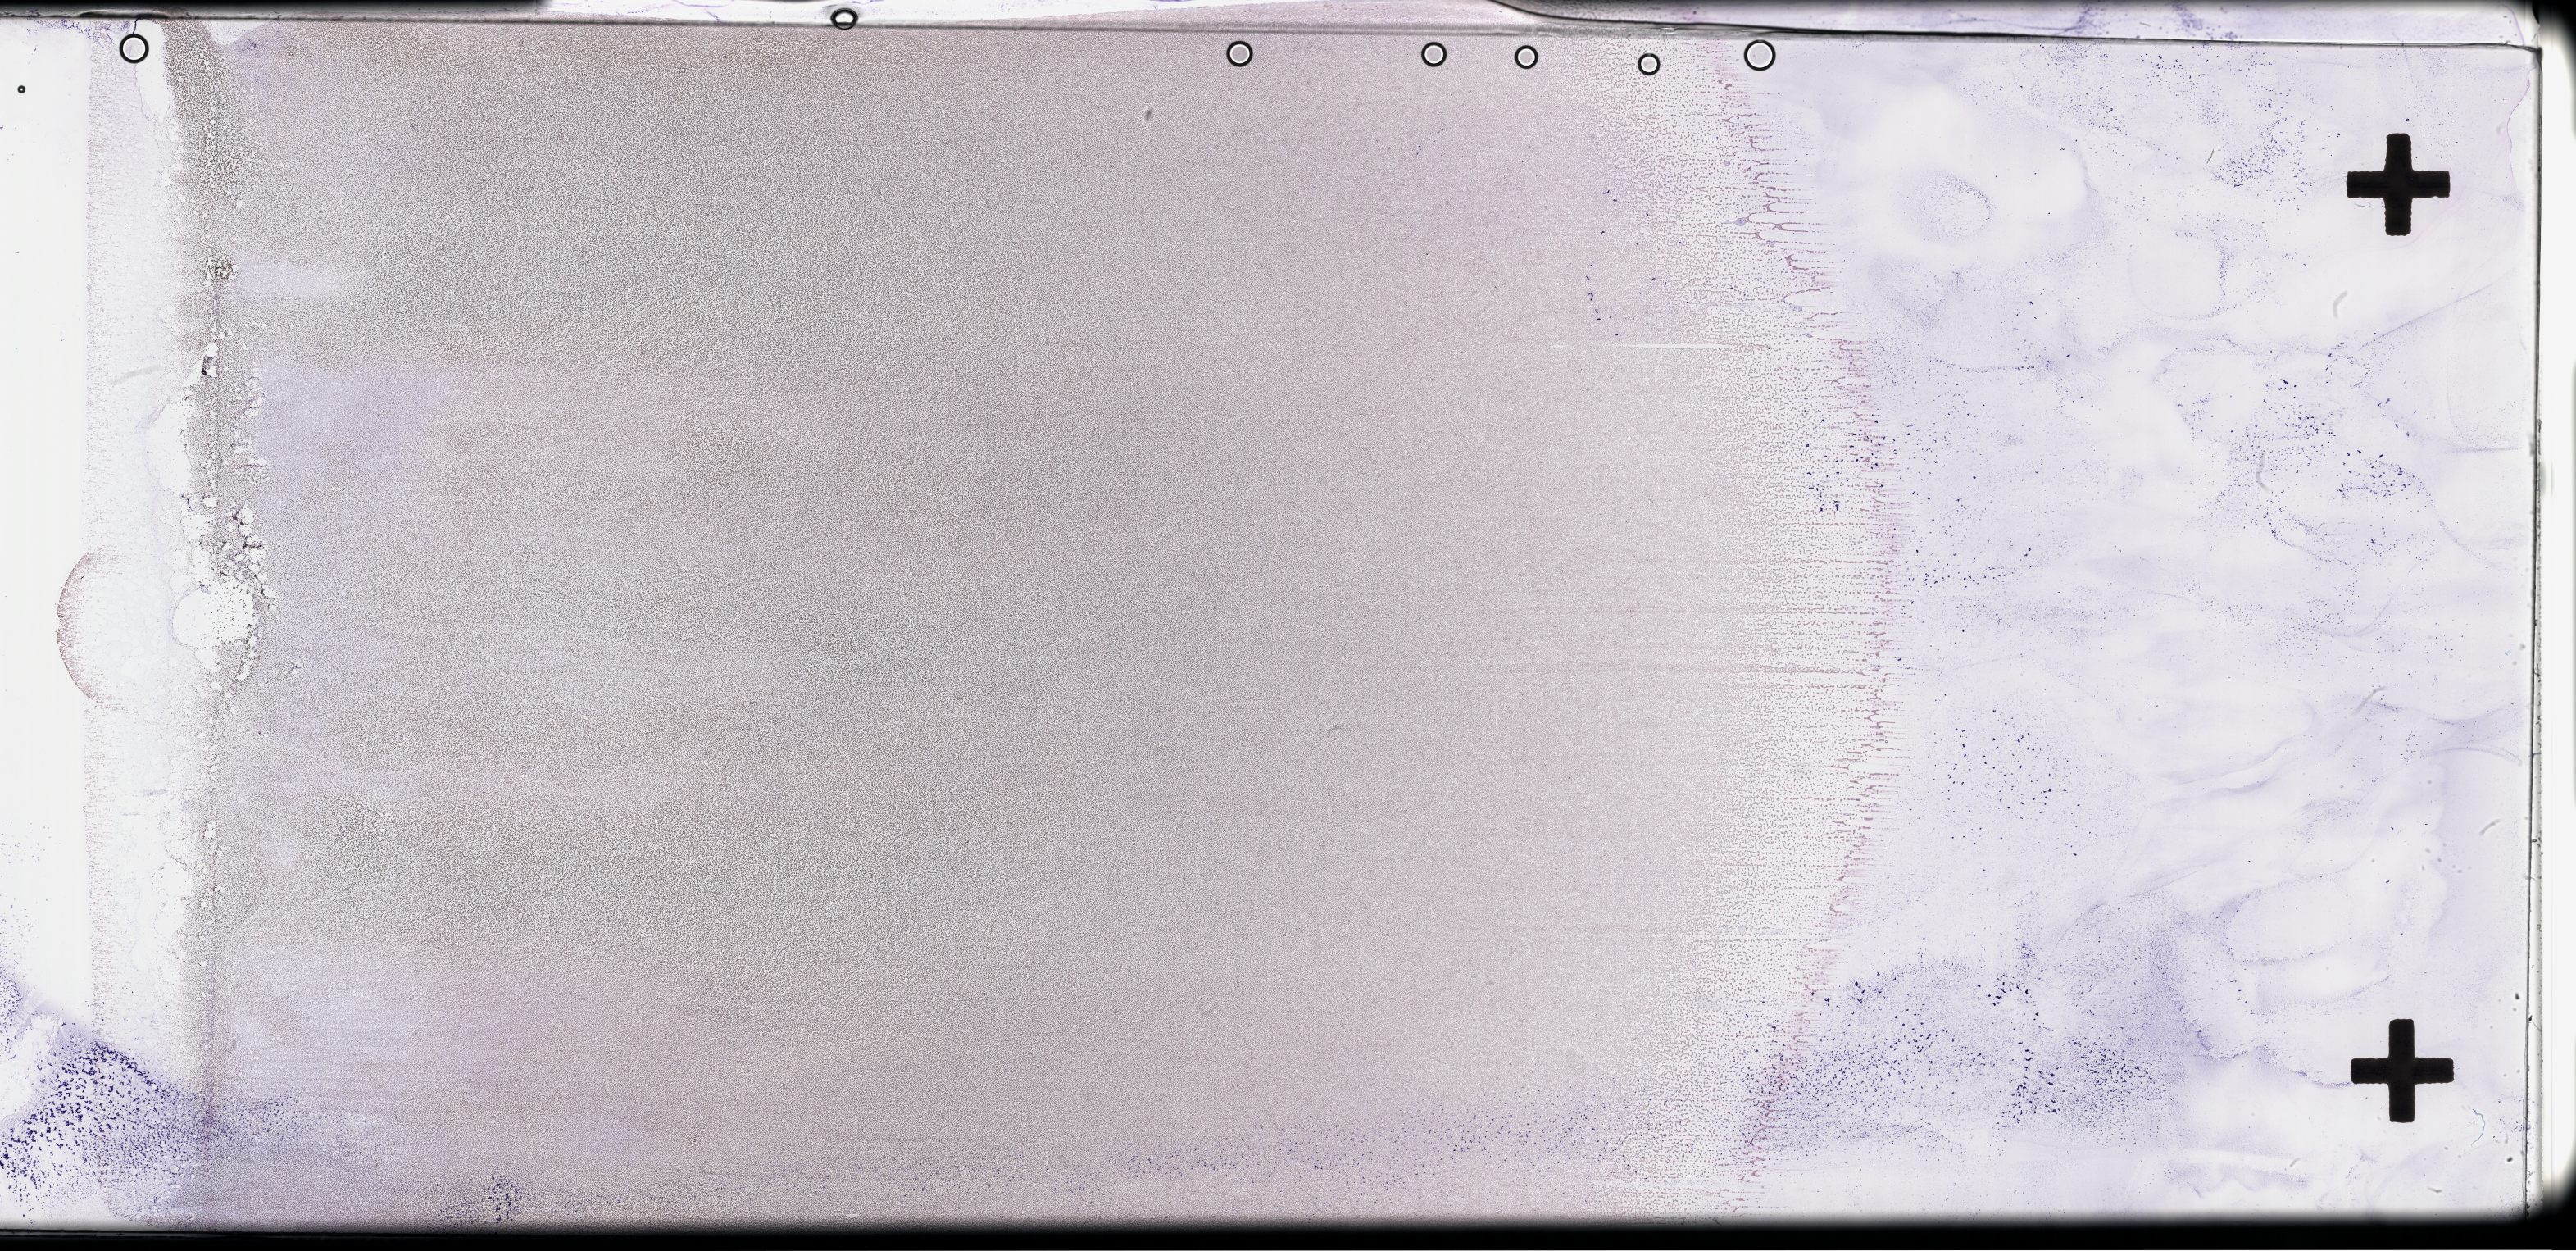
Wright–Giemsa-stained whole blood smear, whole-slide image — low-resolution overview of the scanned area, about 50.8 x 24.6 mm. Smear from an EDTA sample. Specimen time point: collected at baseline (before treatment). Female patient.
Patient diagnosis: Plasma Cell Myeloma.